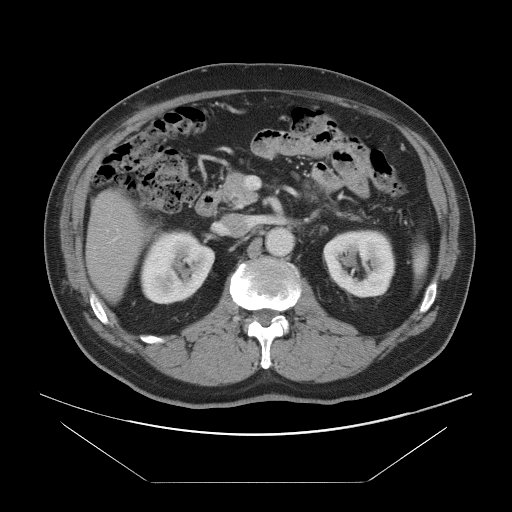
Contrast-enhanced abdominal CT, one axial slice; position 42 of 97 along the scan axis; 120 kVp; intravenous contrast given; soft-tissue window (W 400 / L 40 HU); 5 mm slice thickness; 512 × 512 image matrix. Male patient, age 62 years. Case-level facts recorded for this patient, not image findings: diagnosis: colorectal cancer liver metastases, imaged before liver resection; multiple liver metastases: no; largest metastasis: 7 cm; disease in both lobes: yes.
Structures marked on this image (outlined manually by an expert reader):
- hepatic veins: box from (x=106, y=229) to (x=109, y=232) px
- liver: (x=88, y=192)–(x=144, y=299)
- planned liver remnant (the part of the liver to remain after resection): (x=88, y=192)–(x=143, y=299)
- portal vein (with intrahepatic branches): (x=112, y=236)–(x=120, y=241)